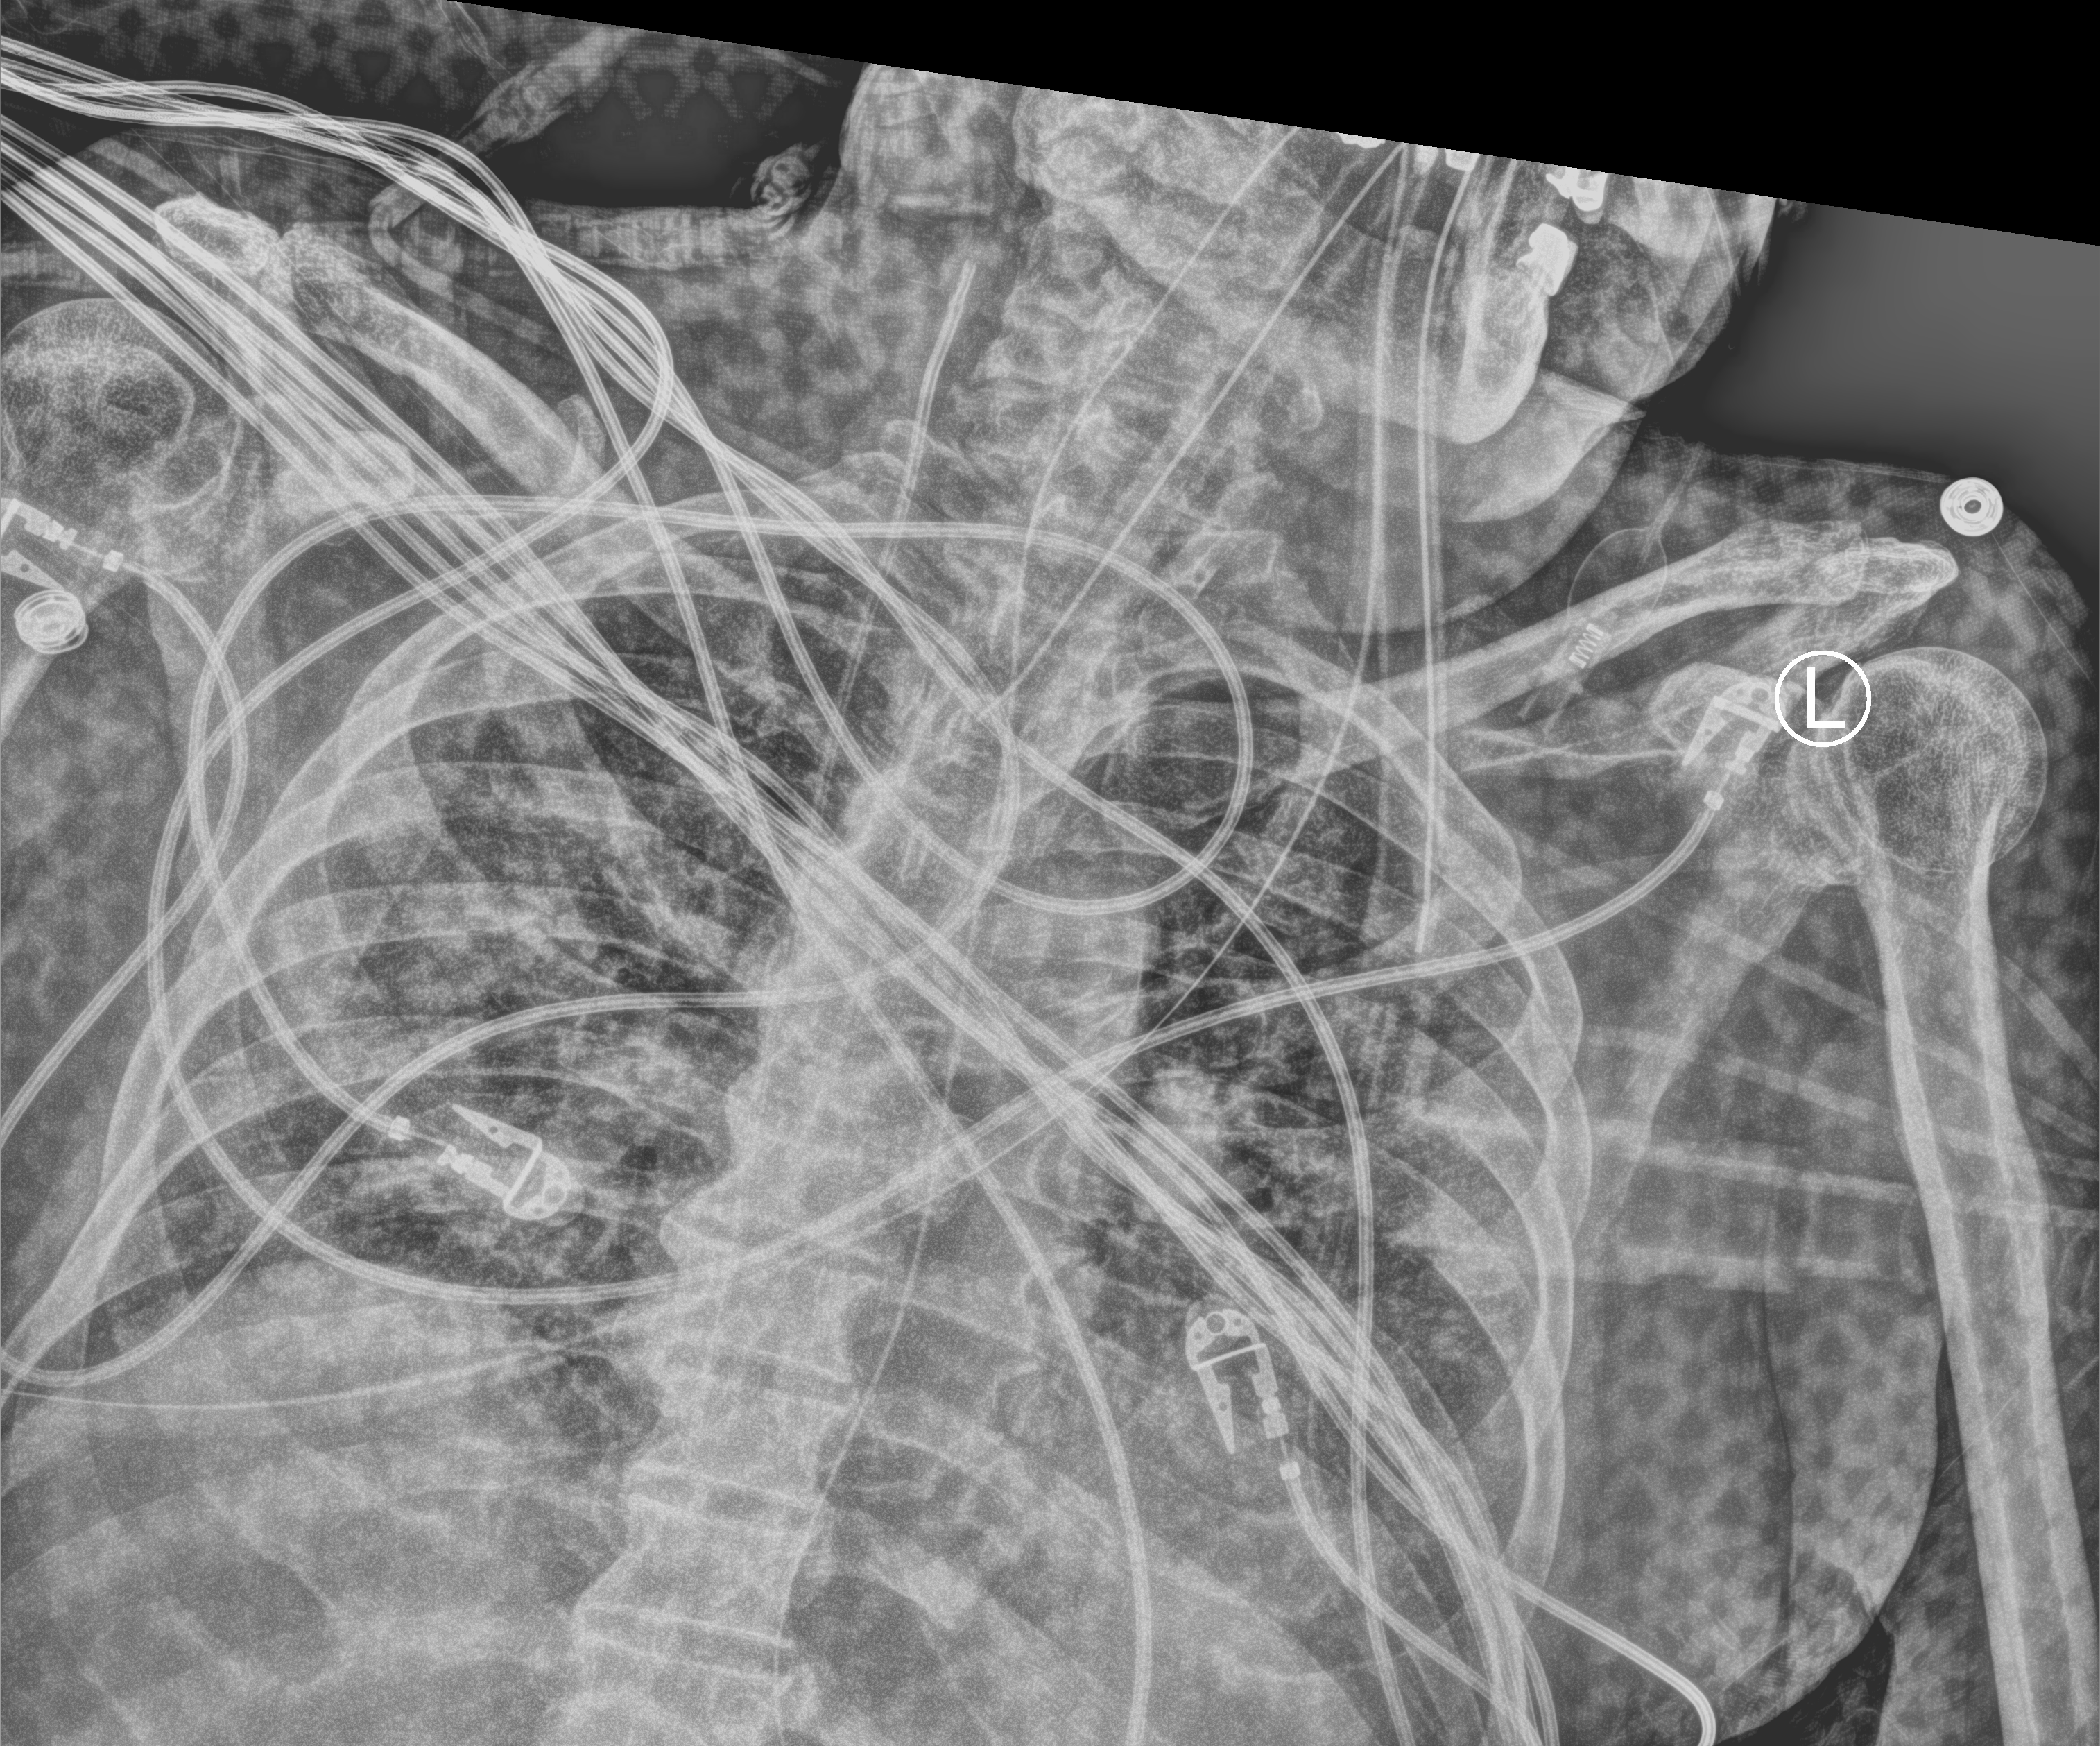
Bedside chest radiograph (computed radiography); anteroposterior (AP) projection. Male patient hospitalised with COVID-19, age 75–90 years.
Admission-level facts for this patient (not findings on this image; timing relative to this image not recorded): other chronic lung disease (admission record): no.